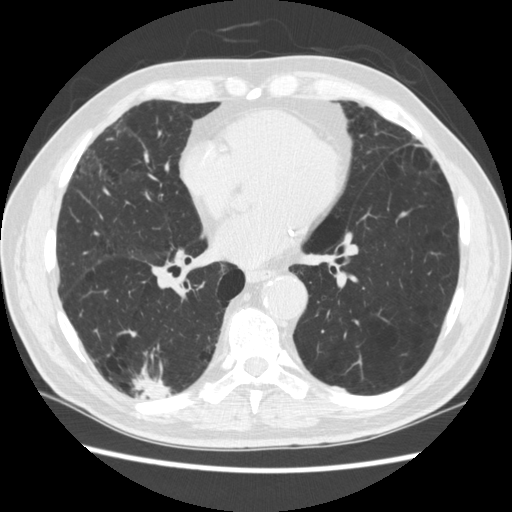
Low-dose screening chest CT, axial slice. Third annual screen. Lung window (W 1500 / L -600 HU). 1.25 mm slice thickness. Standard (soft-tissue) reconstruction kernel (STANDARD). Slice 149 of 266 in the series. Male, age 70 years at enrolment. Former smoker at enrolment.
• Expert reader's lesion annotation, bounding box [x1, y1, x2, y2] px = [124, 360, 182, 418].
• The screening reader recorded 4 non-calcified nodules or masses ≥4 mm on this exam; which of them this box marks is not recorded.
• Lung cancer was diagnosed 253 days after this screen: squamous cell carcinoma, NOS, right upper lobe, poorly differentiated (G3), stage IV (AJCC 6th edition).